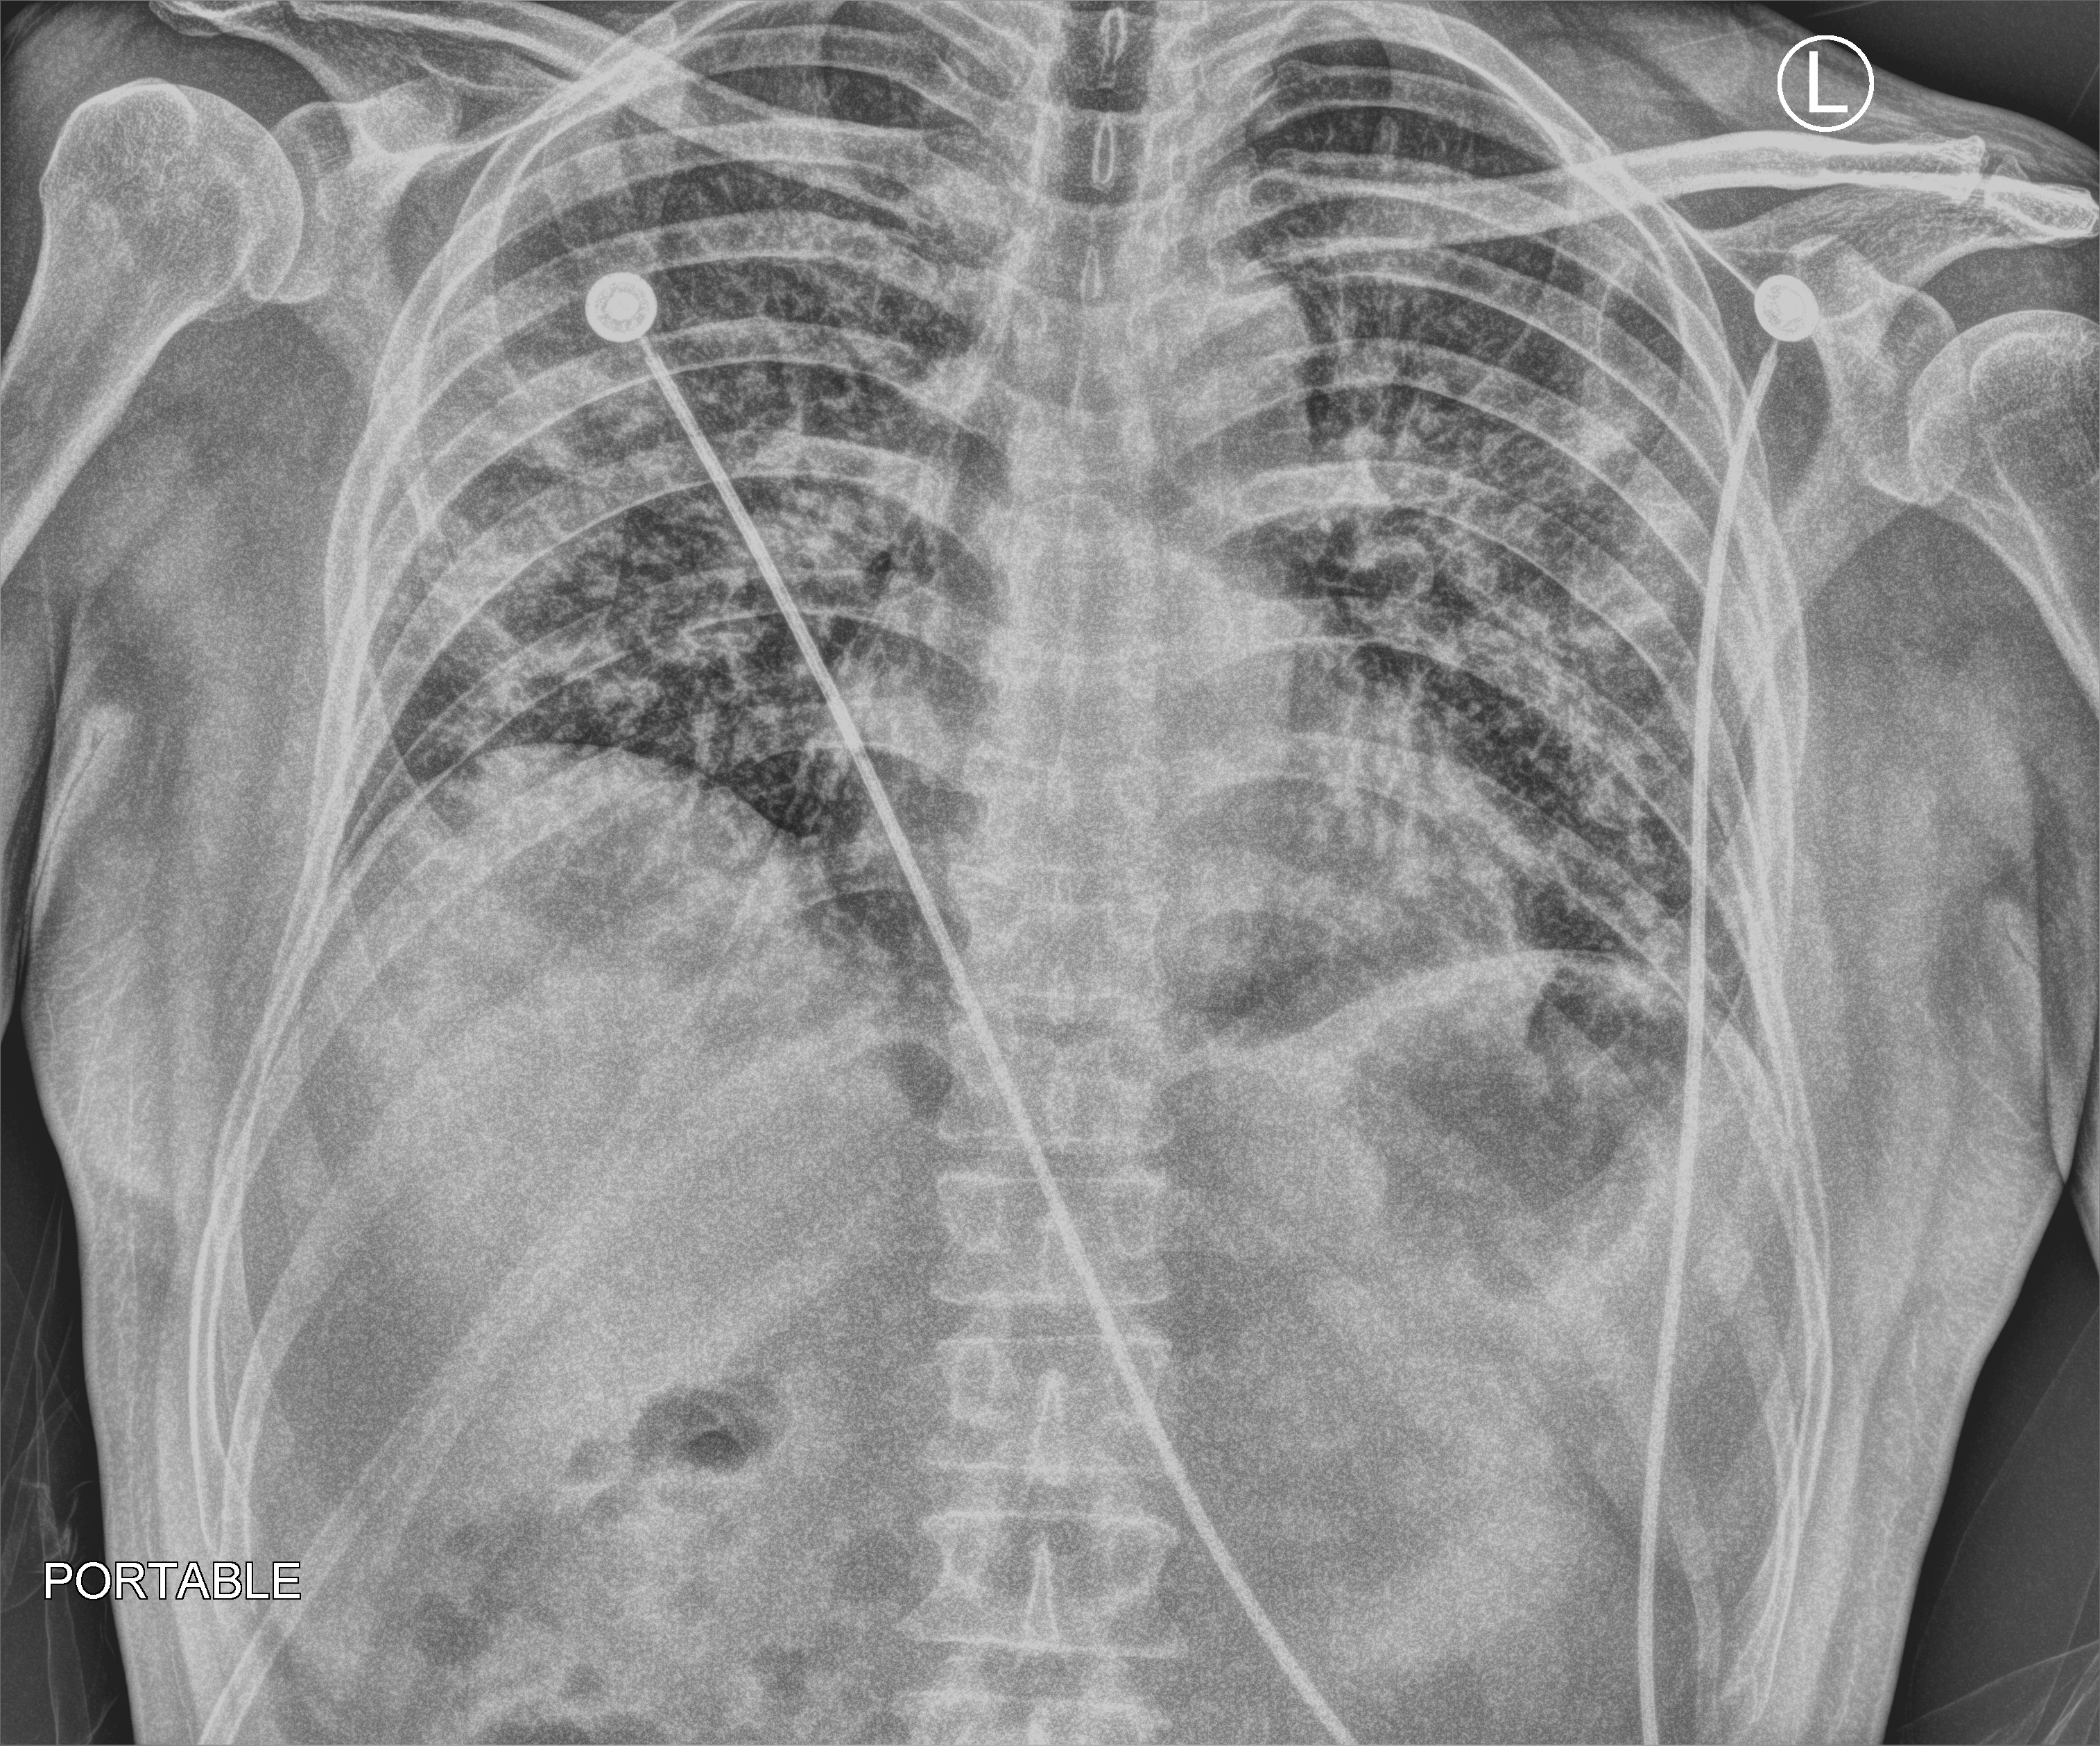
Portable chest radiograph, anteroposterior (AP) projection. Patient hospitalised with COVID-19; male, aged 18–59 years.
Admission-level facts for this patient (not findings on this image; timing relative to this image not recorded): admitted to intensive care during this hospital stay: no; mechanically ventilated during this hospital stay: no.